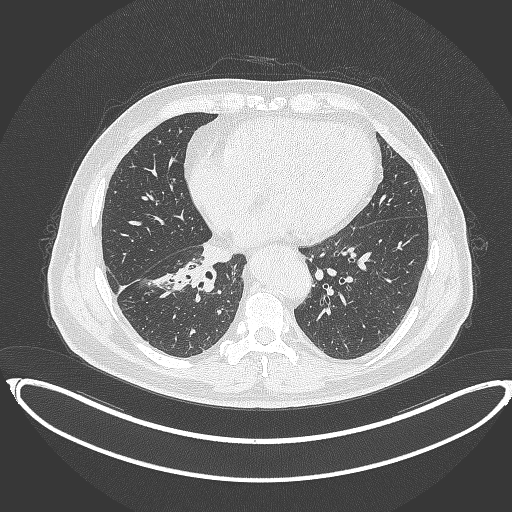
Chest CT, one axial slice; slice 158 of 387 in the series (ordered by position); reconstruction kernel B70f; lung window (W 1500 / L -600 HU); 1 mm slice thickness; 512 × 512 image matrix, field of view 448 × 448 mm. Patient: male, 61 years. Case-level facts recorded for this patient, not image findings: clinical TNM (as recorded): T1b N1 M0.
Annotated regions visible in this slice (bounding box drawn by a radiologist):
- lung tumour (recorded histology: squamous cell carcinoma): bounding box [x1, y1, x2, y2] px = [171, 259, 218, 291]